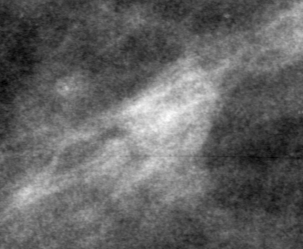
Crop from a digitized film mammogram around one marked abnormality; right breast; MLO view.
Mass, shape lobulated, margins obscured; BI-RADS assessment category 0; pathology (as recorded): benign.